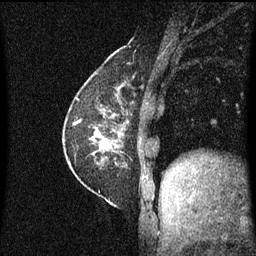
Breast MRI (dynamic contrast-enhanced), one sagittal slice; position 20 of 60 along the scan axis; dynamic contrast-enhanced series, image 2 of 3 at this slice position (ordered by acquisition); 1.5 T; TE 4.2 ms, TR 8.4 ms; 2 mm slice thickness; 256 × 256 image matrix, field of view 200 × 200 mm. Female patient, age 60 years.
Structures marked on this image (semi-automatic segmentation, software-assisted and operator-edited):
- analysis volume of interest (the breast-tissue region the enhancement analysis was run in; not a lesion): bounding box (x1, y1, x2, y2) in pixels: (69, 66, 132, 193)
- tumour enhancement mask (voxels above the 70 % enhancement threshold inside the analysis volume of interest): (69, 84, 129, 165)